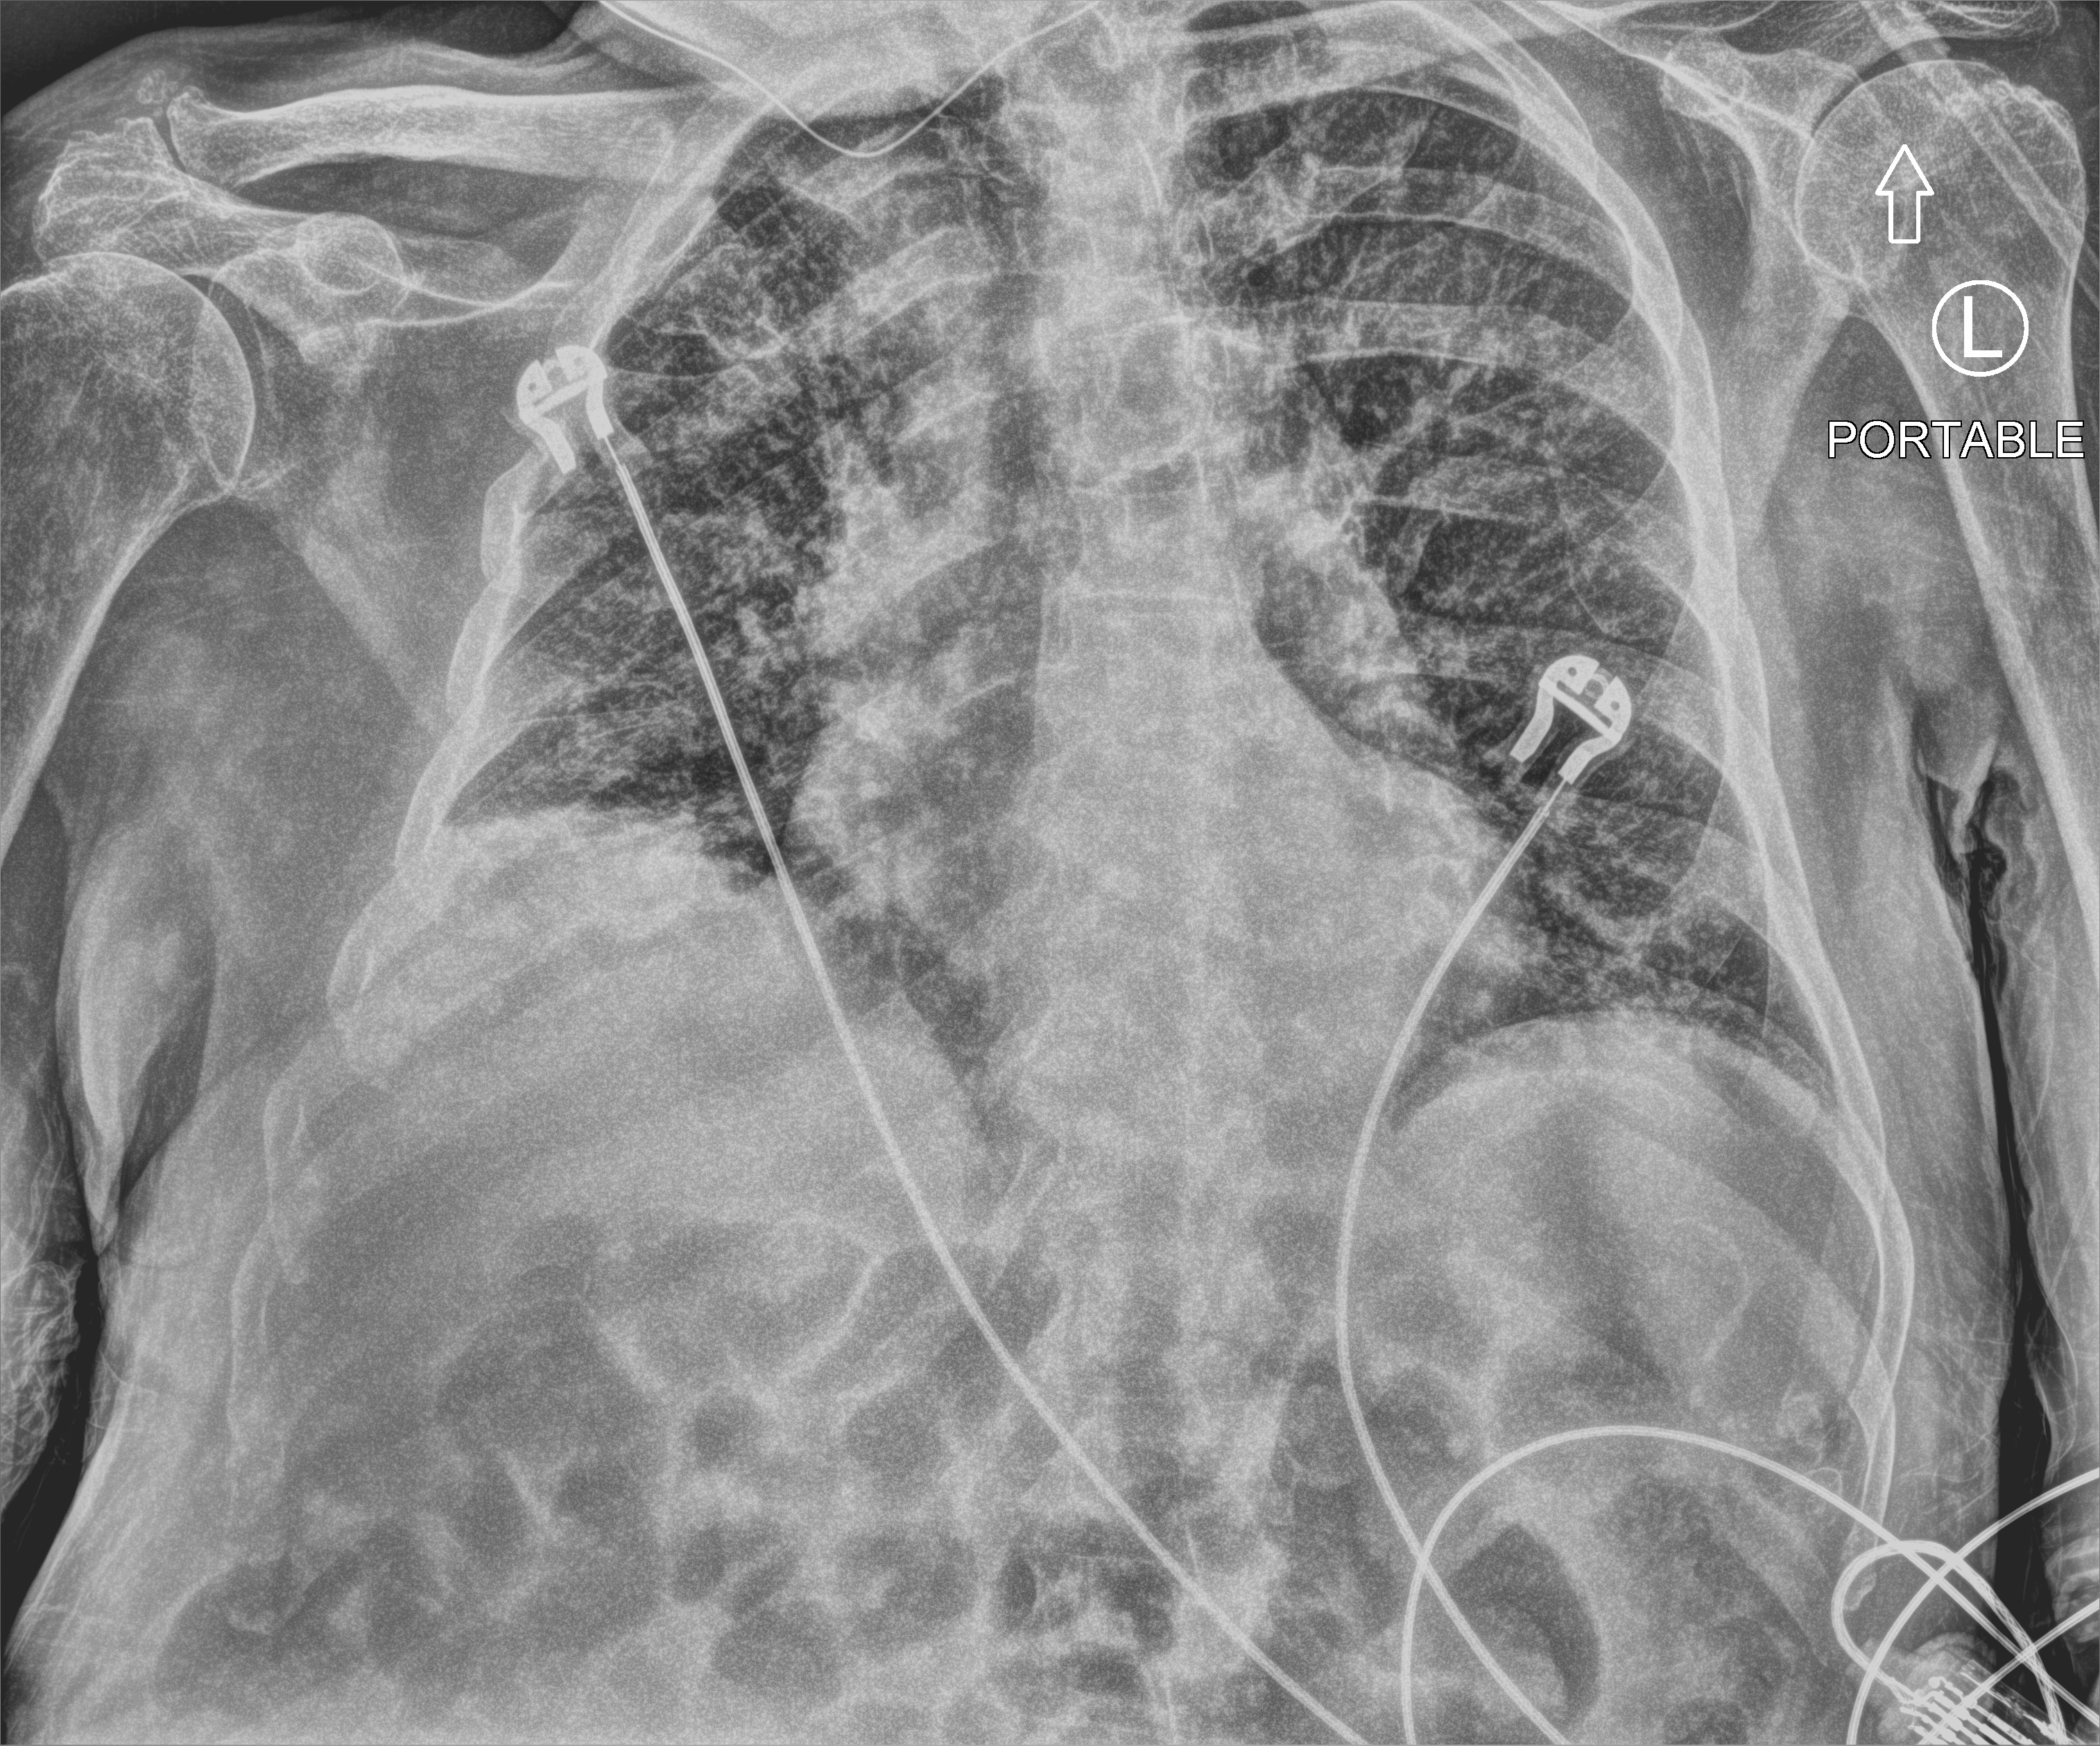
Portable chest radiograph, anteroposterior (AP) projection. Patient hospitalised with COVID-19; male, aged 75–90 years.
Hospital-stay facts (about this admission, not read from this image; timing relative to this image not recorded):
- mechanically ventilated during this hospital stay: yes